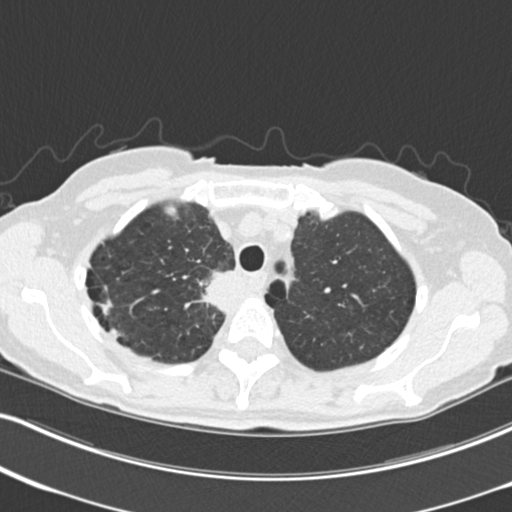
Axial slice from a low-dose chest CT screening exam, third annual screen, lung window (W 1500 / L -600 HU), 2 mm slice thickness, standard (soft-tissue) reconstruction kernel (B30f), 120 kVp. Female, age 68 years at enrolment. Current smoker at enrolment.
- Expert reader's lesion annotation, box from (x=199, y=264) to (x=251, y=319) px.
- Screening reader's record for this exam (one nodule recorded; not confirmed to be the boxed lesion): non-calcified nodule or mass ≥4 mm, right upper lobe, 31 × 29 mm, poorly defined margins, soft tissue attenuation, pre-existing on the prior screen: no.
- Official screen result: positive, other.
- Later outcome: lung cancer diagnosed 79 days after this screen — squamous cell carcinoma, NOS, right upper lobe, mediastinum, poorly differentiated (G3), stage IIIB (AJCC 6th edition), 43 mm at pathology.